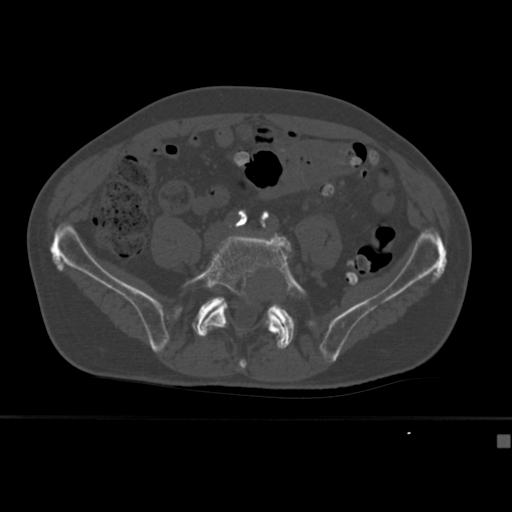
CT including the spine, one axial slice; slice 84 of 430 in the series (ordered by position); 120 kVp; bone window (W 1800 / L 400 HU); 512 × 512 image matrix, field of view 337 × 337 mm. Male patient, age 64 years. From the clinical record (not read from this slice): primary cancer: uterus; vertebrae with lytic lesions (as recorded): T1, T4, T5, T7, L5.
Outlined on this slice (semi-automatically segmented with operator editing):
- L5 vertebra: box from (x=181, y=234) to (x=307, y=349) px